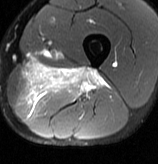
MRI of an extremity soft-tissue mass, one axial slice; position 29 of 70 along the scan axis; T2-weighted fat-saturated; MR volume resampled by the dataset authors to the PET/CT grid (not the native acquisition matrix); 3.27 mm slice thickness; 158 × 164 image matrix, field of view 154 × 160 mm. Male patient. From the clinical record (not read from this slice): histological type: extraskeletal osteosarcoma; grade: high; site of the primary tumour: left adductur.
Outlined on this slice (expert contour drawn on MRI and transferred to this co-registered scan by the dataset authors):
- gross tumour volume (mass): box from (x=19, y=59) to (x=110, y=118) px